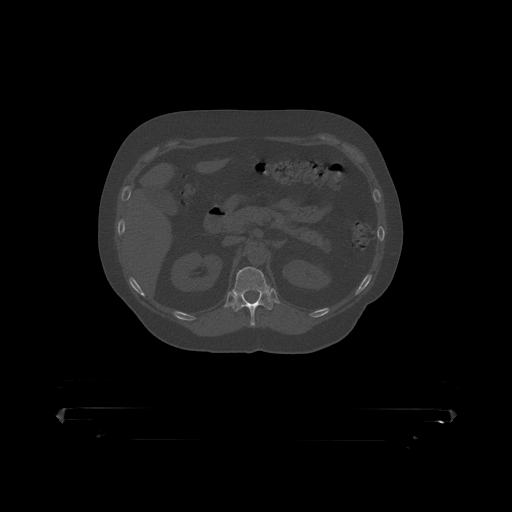
CT including the spine, one axial slice. Reconstruction kernel STANDARD. Bone window (W 1800 / L 400 HU). 512 × 512 image matrix. Patient: male, 60 years. Case-level facts recorded for this patient, not image findings: primary cancer: prostate.
Outlined on this slice (semi-automatic segmentation, software-assisted and operator-edited):
- T12 vertebra: bounding box [x1, y1, x2, y2] px = [231, 267, 274, 319]